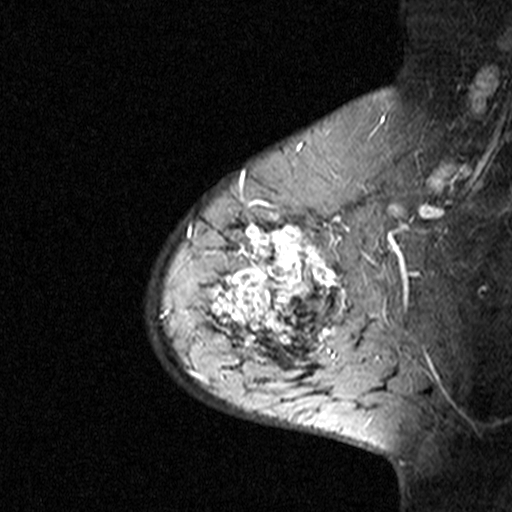
Breast MRI (dynamic contrast-enhanced), one sagittal slice; position 31 of 44 along the scan axis; dynamic contrast-enhanced study with each time point stored as its own series, time point 3 of 4 at this slice position (ordered by acquisition time); 1.5 T; TE 4.5 ms, TR 11 ms; 3 mm slice thickness; 512 × 512 image matrix, field of view 200 × 200 mm. Patient: female, 65 years. Case-level facts recorded for this patient, not image findings: setting: breast cancer imaged before/during neoadjuvant chemotherapy; receptor status: HER2-positive.
Outlined on this slice (semi-automatically segmented with operator editing):
- analysis volume of interest (the breast-tissue region the enhancement analysis was run in; not a lesion): bounding box (x1, y1, x2, y2) in pixels: (182, 190, 353, 361)
- tumour enhancement mask (voxels above the 90 % enhancement threshold inside the analysis volume of interest): (188, 203, 340, 346)